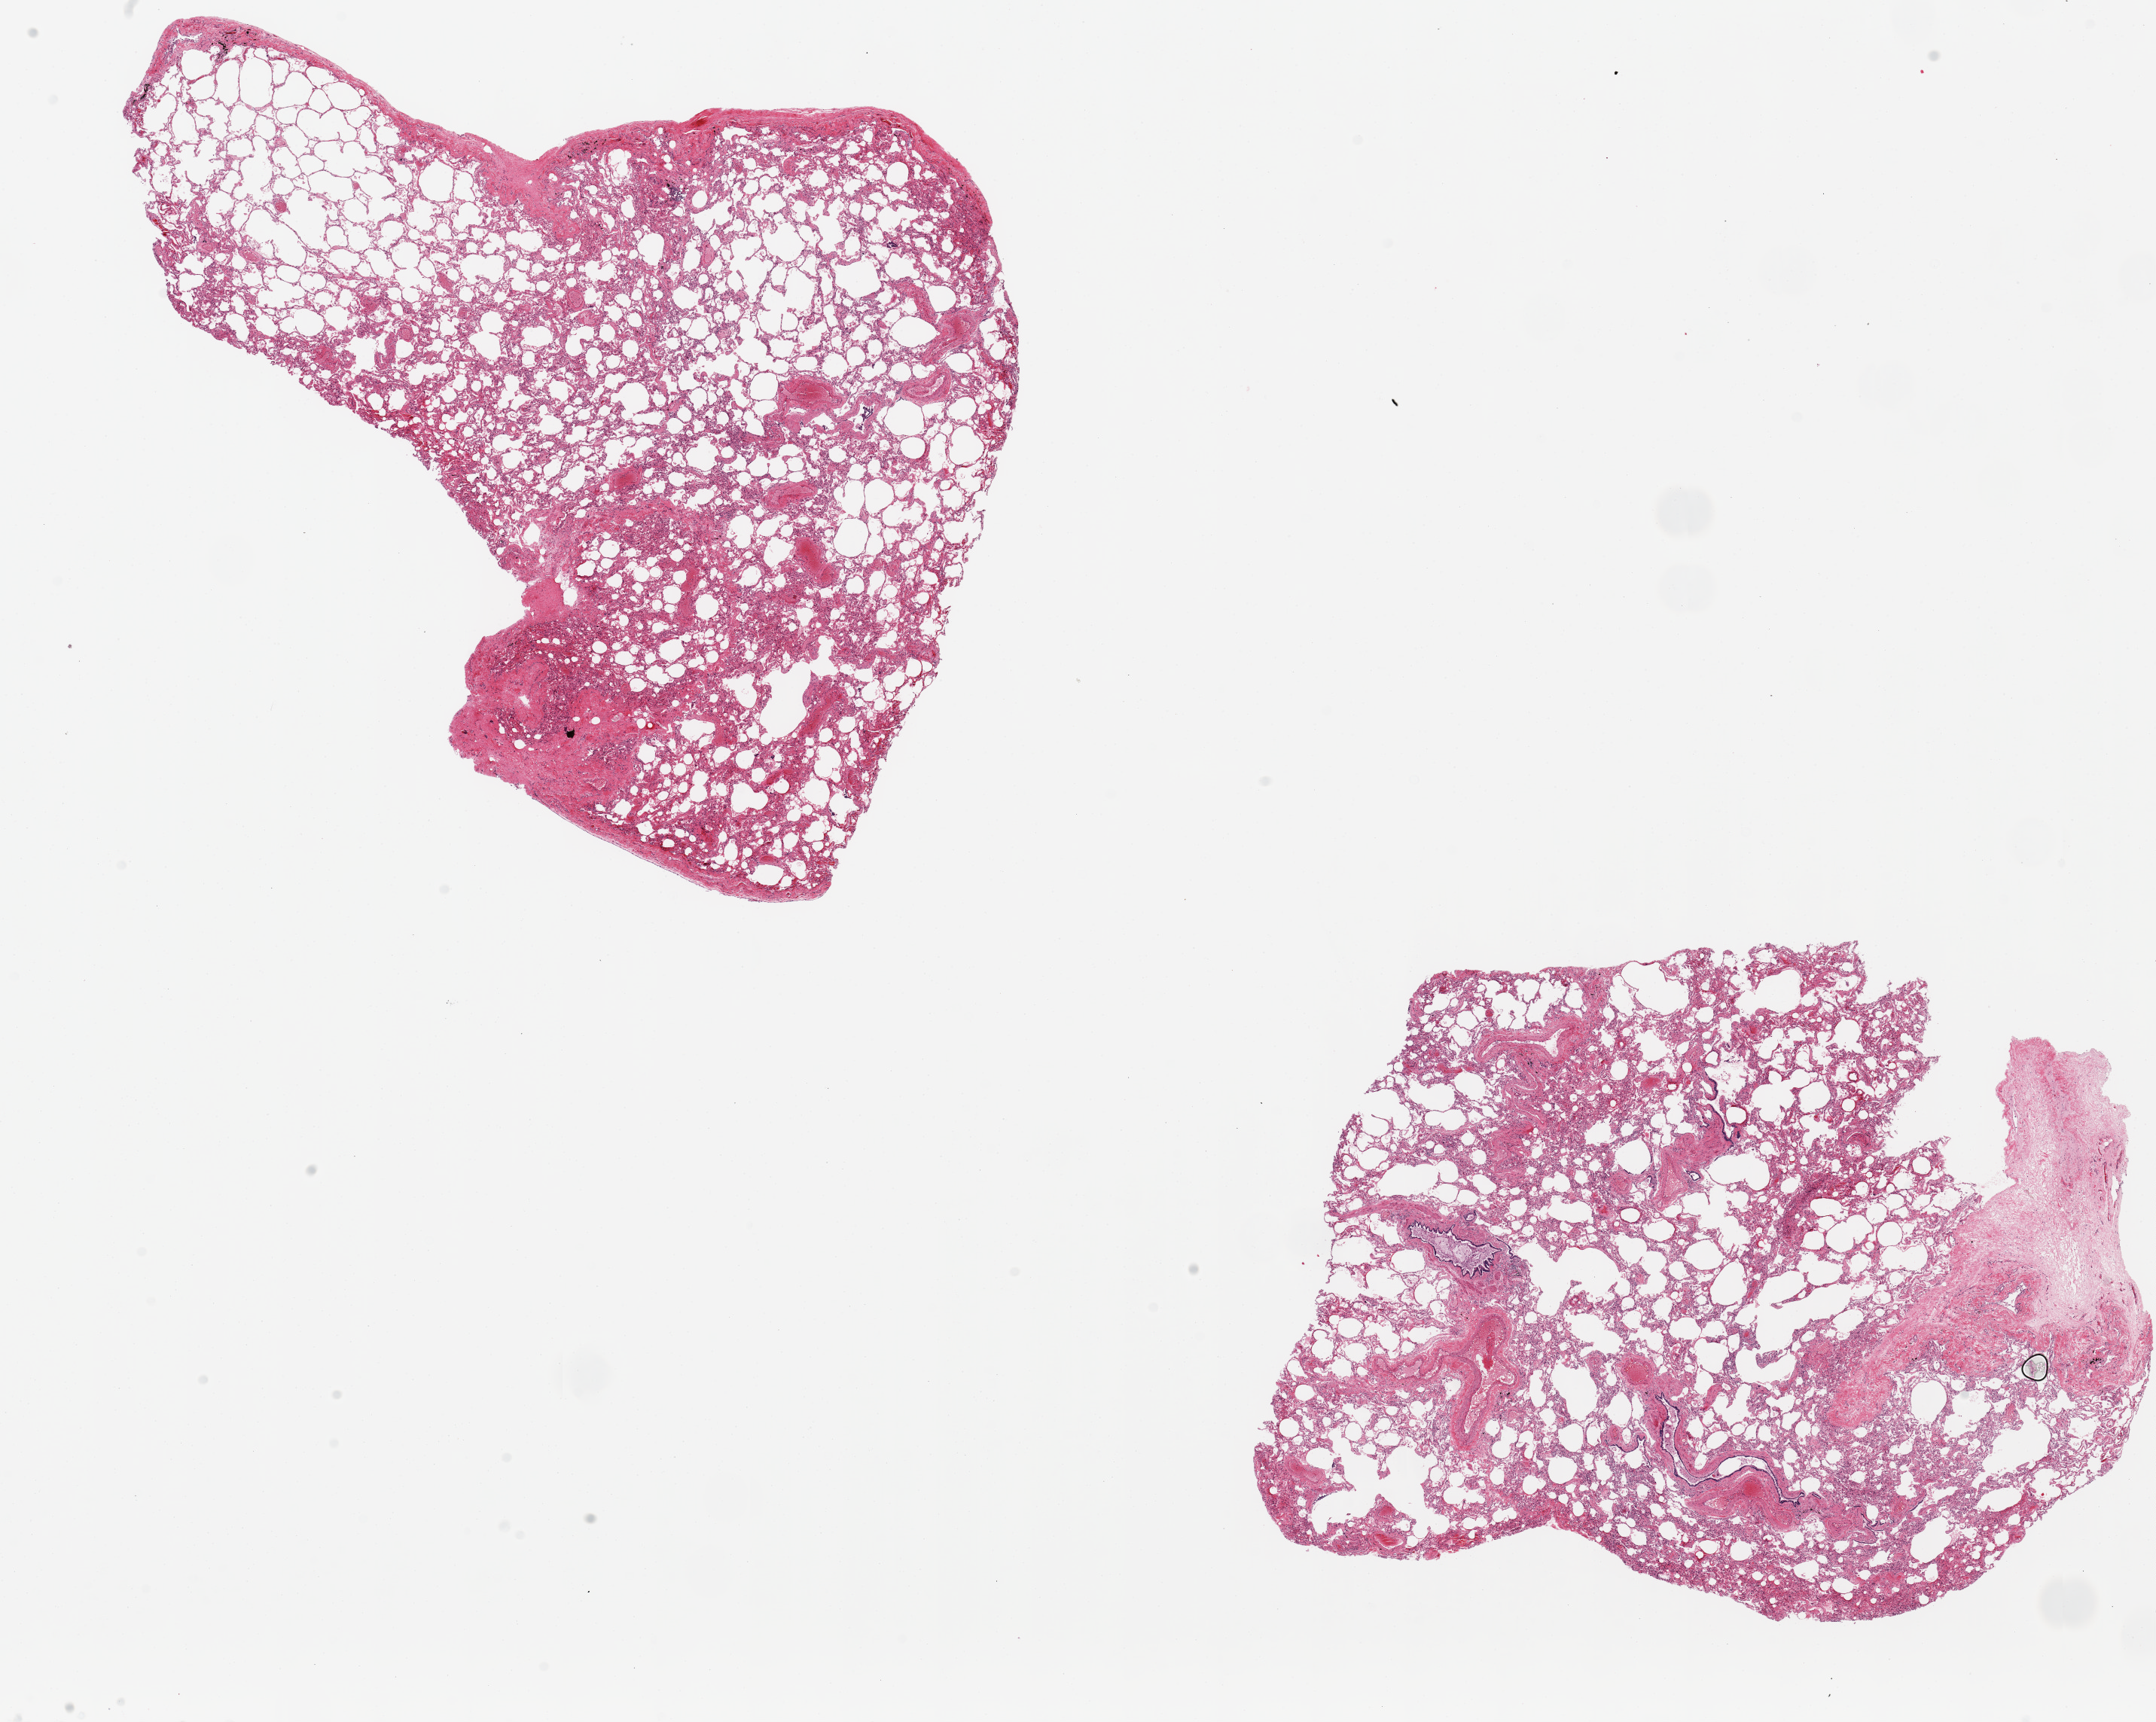
Haematoxylin and eosin whole-slide image, a low-resolution overview of the entire scanned area, about 22.6 x 18.1 mm. Donor: female.
Specimen: PAXgene-fixed paraffin-embedded (PFPE) section; section of lung (target tissue); donor tissue sample.